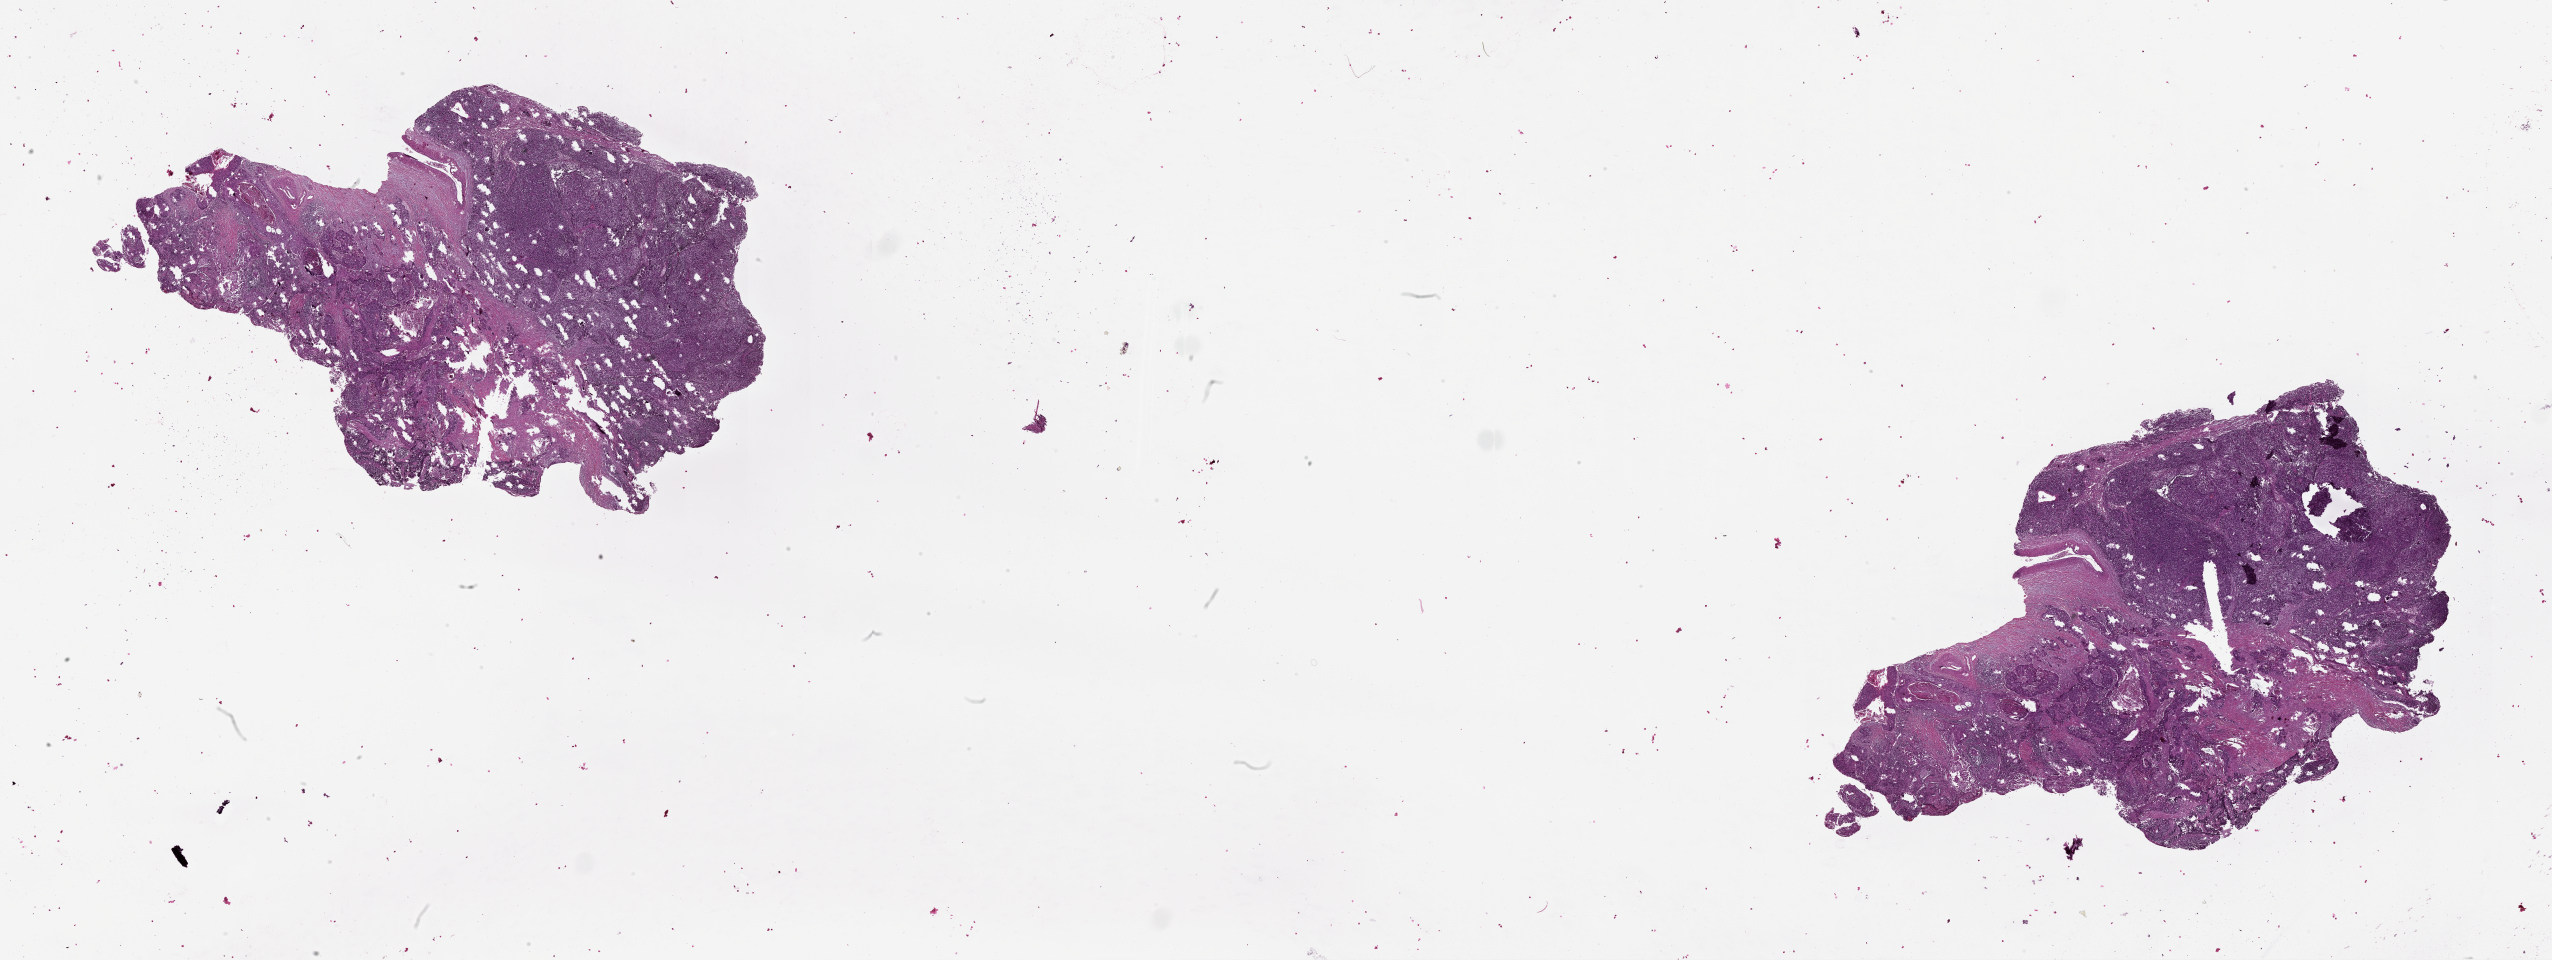
Whole-slide histology image, Hematoxylin and eosin (H&E) stained, low-resolution overview of the scanned area, about 41.1 x 15.5 mm (from a 20x scan). Lung, tumour tissue. Patient: male, age 65 years.
Patient diagnosis (cohort enrolment): squamous cell carcinoma (lung).